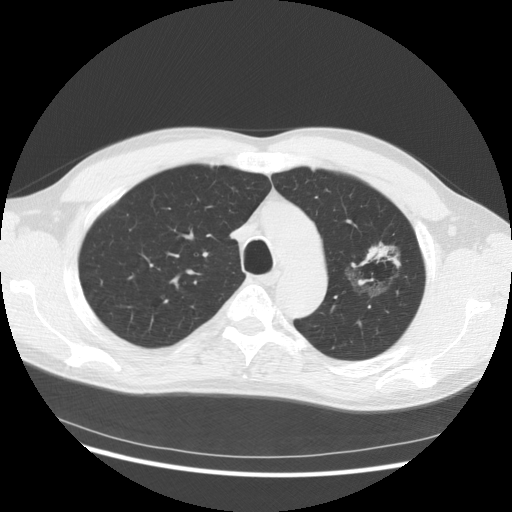
Low-dose screening chest CT, axial slice. Third annual screen. Lung window (W 1500 / L -600 HU). 2.5 mm slice thickness. Standard (soft-tissue) reconstruction kernel (STANDARD). Slice 106 of 145 in the series. Male participant, aged 61 years at enrolment. Former smoker at enrolment.
Expert-annotated lung lesion, bounding box <332,232,409,312> (left, top, right, bottom; pixels). Screening reader's record for this exam (one nodule recorded; not confirmed to be the boxed lesion): non-calcified nodule or mass ≥4 mm, left upper lobe, 37 × 33 mm, poorly defined margins, mixed attenuation, pre-existing on the prior screen: yes; interval growth: yes. Lung cancer was diagnosed 361 days after this screen: bronchiolo-alveolar adenocarcinoma, NOS, left upper lobe, well differentiated (G1), stage IB (AJCC 6th edition), 44 mm at pathology.